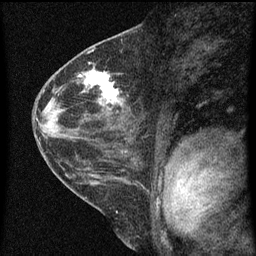
Breast MRI (dynamic contrast-enhanced), one sagittal slice; slice 31 of 60 in the series (ordered by position); dynamic contrast-enhanced series, image 2 of 3 at this slice position (ordered by acquisition); 1.5 T; TE 4.2 ms, TR 8 ms; 2 mm slice thickness; 256 × 256 image matrix, field of view 180 × 180 mm. Patient: female, 48 years.
Annotated regions visible in this slice (semi-automatic segmentation, software-assisted and operator-edited):
- analysis volume of interest (the breast-tissue region the enhancement analysis was run in; not a lesion): box from (x=82, y=68) to (x=126, y=125) px
- tumour enhancement mask (voxels above the 70 % enhancement threshold inside the analysis volume of interest): (x=82, y=72)–(x=123, y=105)